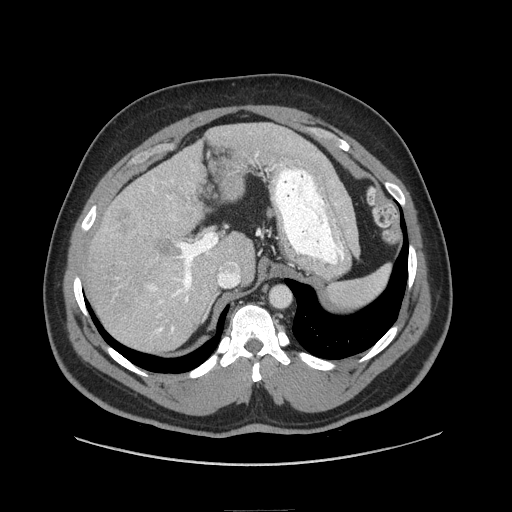
Contrast-enhanced abdominal CT (liver protocol), one axial slice. Position 53 of 87 along the scan axis. 140 kVp. Soft-tissue window (W 400 / L 40 HU). 2.5 mm slice thickness. 512 × 512 image matrix, field of view 440 × 440 mm. Case-level facts recorded for this patient, not image findings: diagnosis: hepatocellular carcinoma (patient treated with transarterial chemoembolisation; whether this scan precedes or follows treatment is not stated here); TNM stage (as recorded): Stage-II; Child-Pugh class: A; tumour differentiation: moderately differentiated; tumour nodularity: uninodular.
Structures marked on this image (semi-automatic segmentation, software-assisted and operator-edited):
- liver parenchyma outside the tumour (the mass and vessels are separate outlines, so this box may not span the whole liver): bounding box (x1, y1, x2, y2) in pixels: (84, 124, 328, 350)
- mass: (101, 197, 180, 260)
- liver vessels: (148, 187, 238, 333)